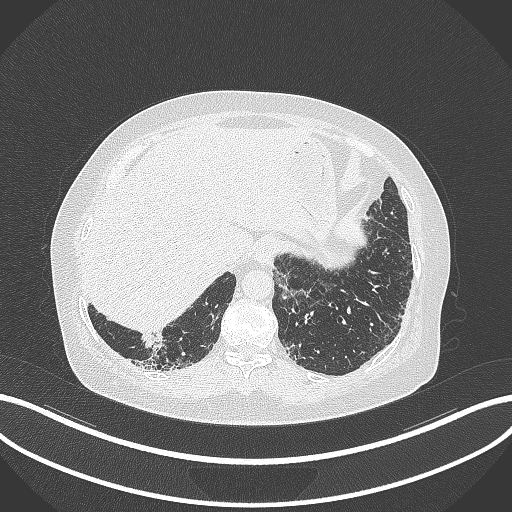
Chest CT, one axial slice. Lung window (W 1500 / L -600 HU). 1 mm slice thickness. 512 × 512 image matrix. Female patient, age 65 years. Case-level facts recorded for this patient, not image findings: clinical TNM (as recorded): T2b N1 M0.
Outlined on this slice (rectangle marked by the reading radiologist):
- lung tumour (recorded histology: adenocarcinoma): bounding box [x1, y1, x2, y2] px = [140, 331, 169, 358]